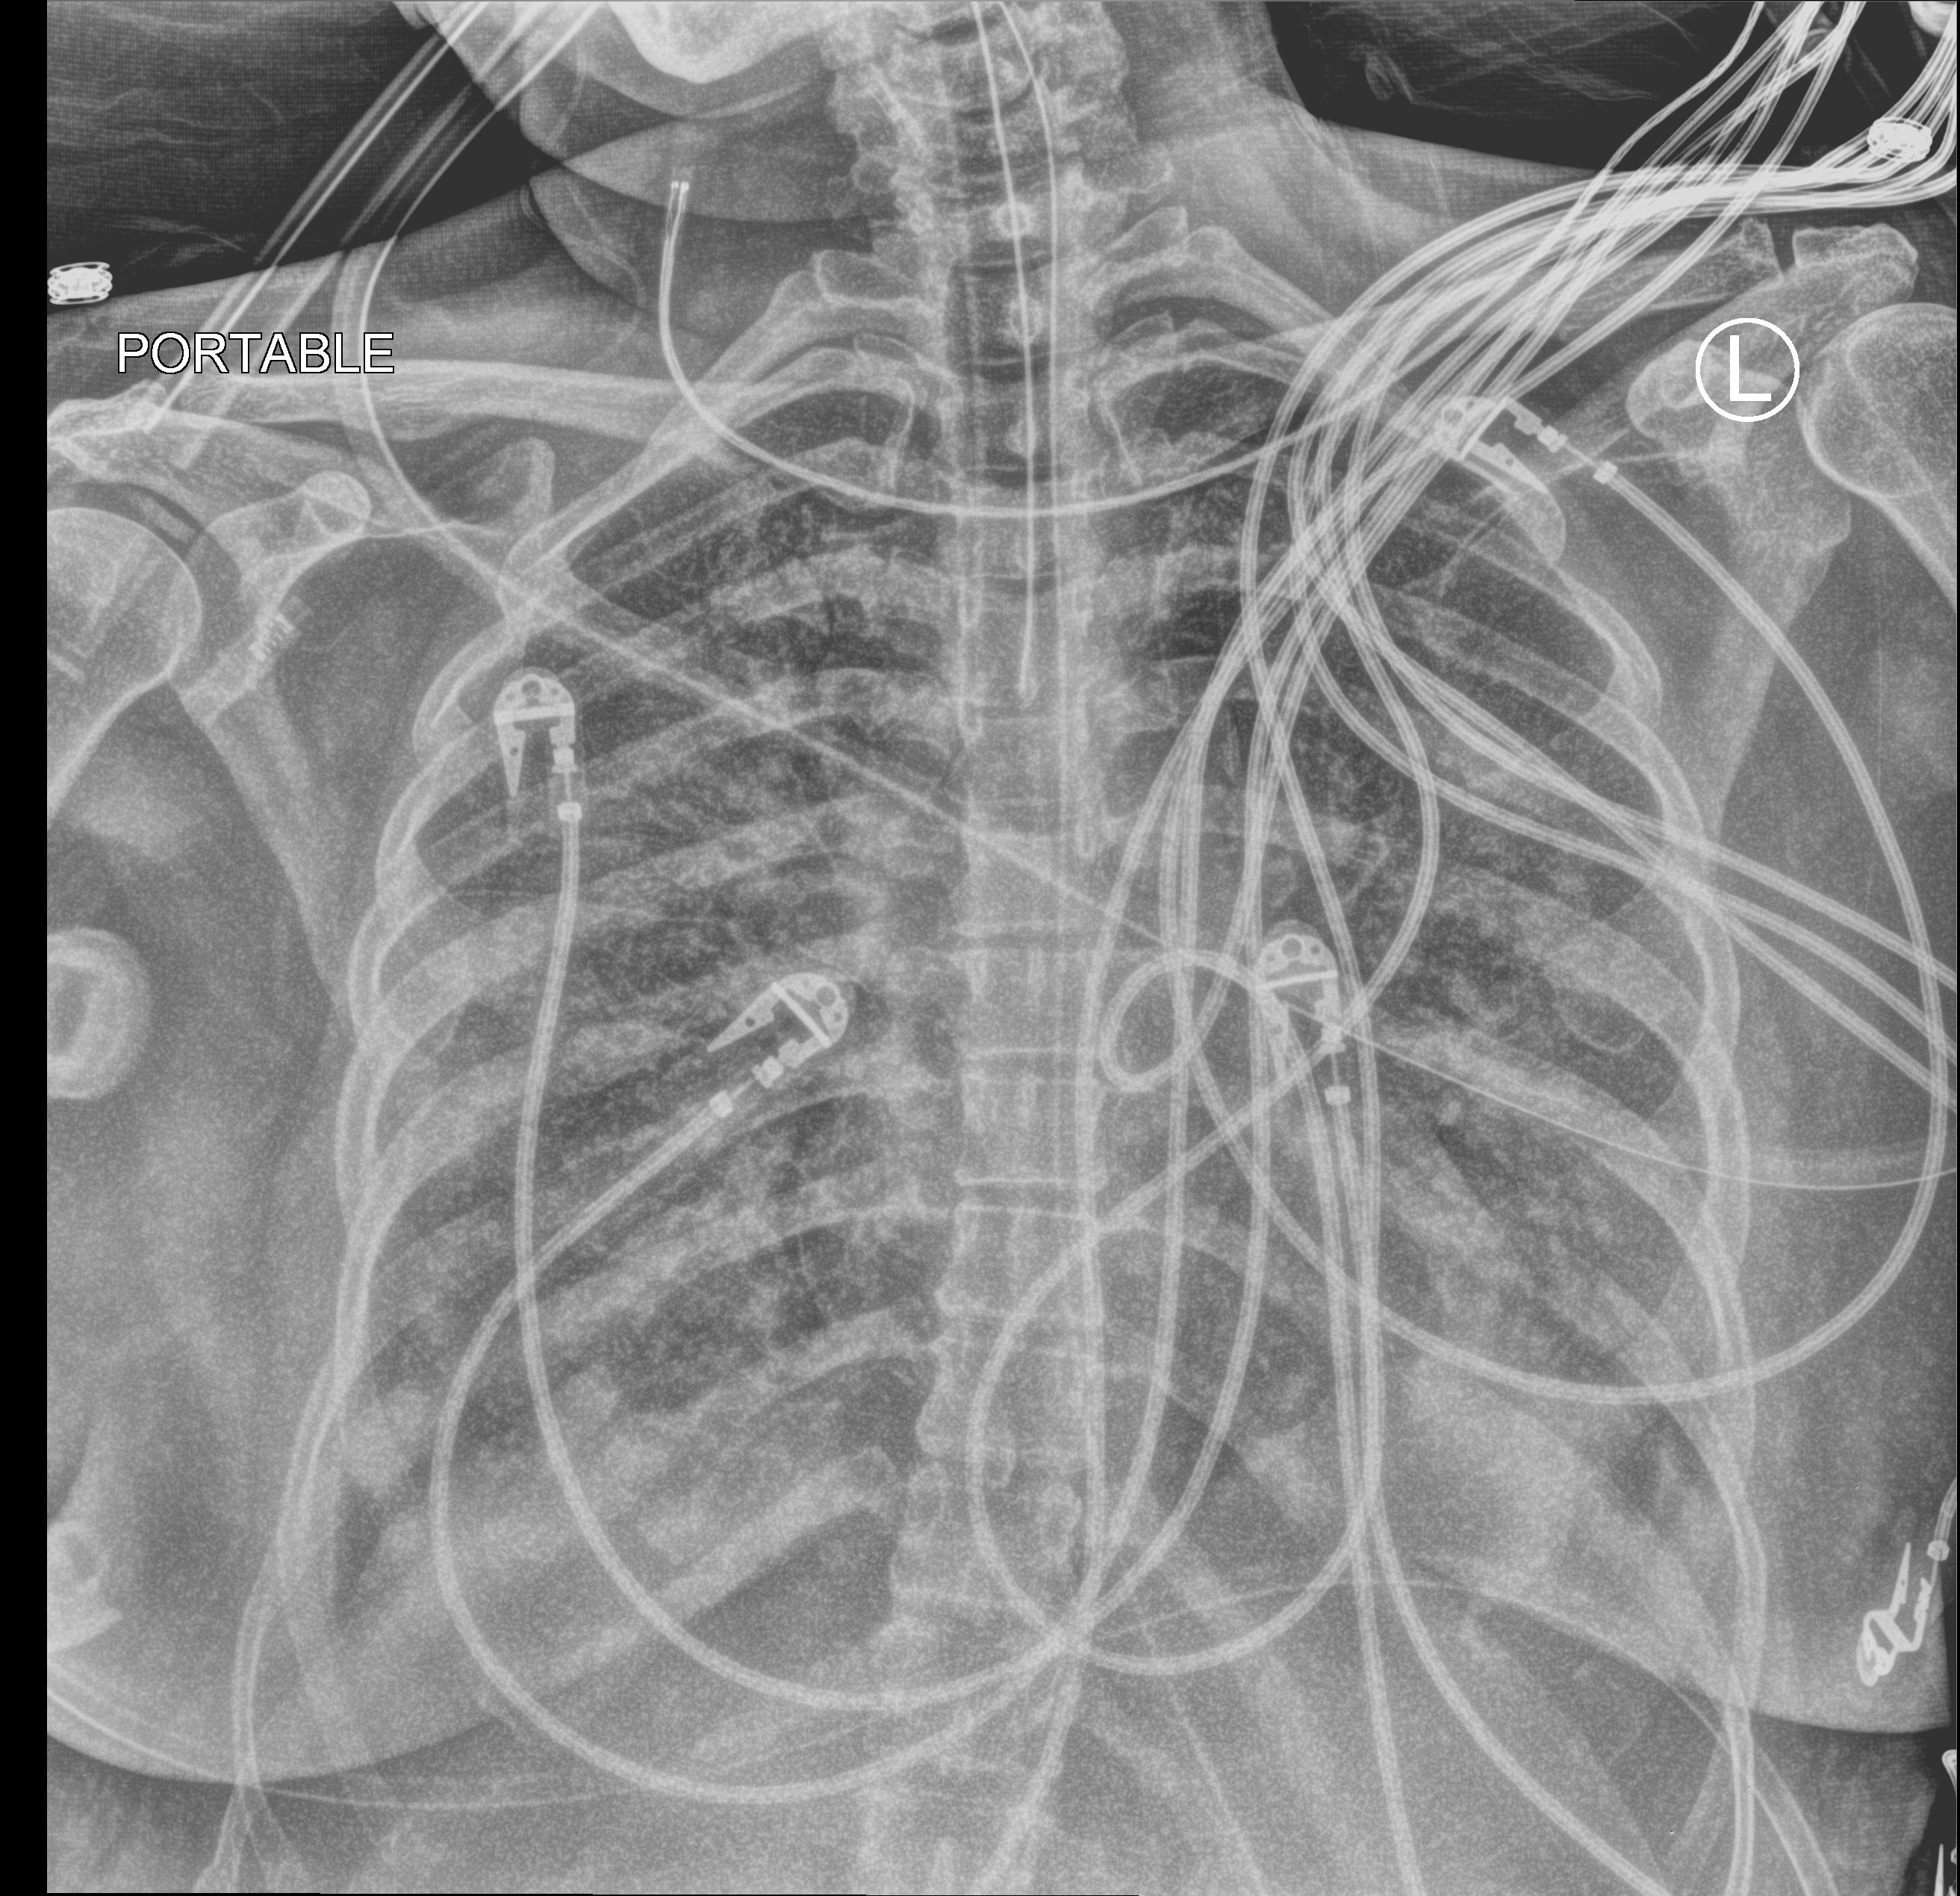
Bedside chest radiograph (computed radiography), anteroposterior (AP) projection. Patient hospitalised with COVID-19; male, aged 18–59 years.
Hospital-stay facts (about this admission, not read from this image; timing relative to this image not recorded):
- other chronic lung disease (admission record): no